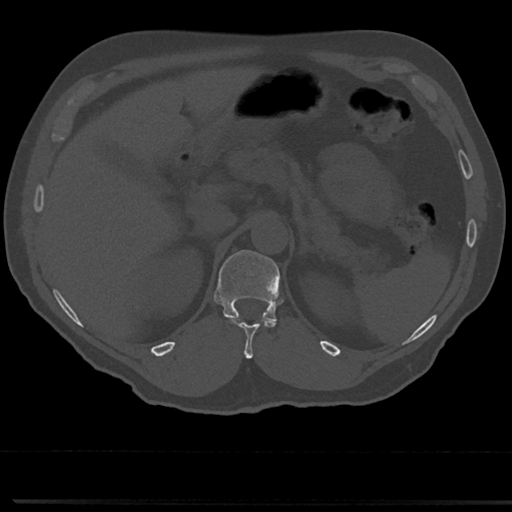
CT including the spine, one axial slice; slice 169 of 817 in the series (ordered by position); reconstruction kernel Br40s/3; 120 kVp; bone window (W 1800 / L 400 HU); 0.5 mm slice thickness; 512 × 512 image matrix. Patient: male, 61 years. From the clinical record (not read from this slice): primary cancer: prostate.
Outlined on this slice (semi-automatically segmented with operator editing):
- T11 vertebra: box from (x=243, y=325) to (x=253, y=358) px
- T12 vertebra: (x=214, y=250)–(x=286, y=337)